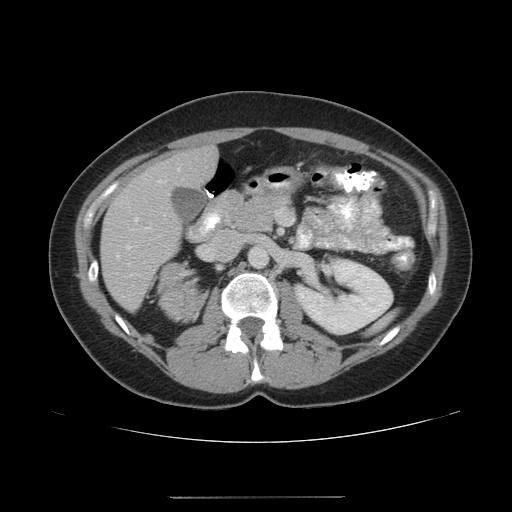
Contrast-enhanced abdominal CT, one axial slice; slice 97 of 161 in the series (ordered by position); 120 kVp; intravenous contrast given; soft-tissue window (W 400 / L 40 HU); 3.75 mm slice thickness; 512 × 512 image matrix, field of view 380 × 380 mm. Female patient. Case-level facts recorded for this patient, not image findings: diagnosis: adrenocortical carcinoma; tumour side: right adrenal; tumour size at pathology: 9 cm; Ki-67 index: 14 %; stage (as recorded): 3.
Annotated regions visible in this slice (semi-automatically segmented with operator editing):
- mass: bounding box <159,263,207,324> (left, top, right, bottom; pixels)